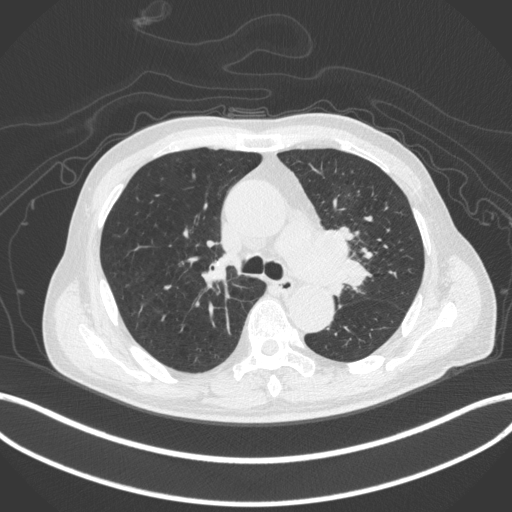
Chest CT, one axial slice; slice 285 of 420 in the series (ordered by position); 120 kVp; lung window (W 1500 / L -600 HU); 1 mm slice thickness; 512 × 512 image matrix, field of view 400 × 400 mm. Patient: male, 77 years. From the clinical record (not read from this slice): clinical TNM (as recorded): T3 N1 M0.
Structures marked on this image (bounding box drawn by a radiologist):
- lung tumour (recorded histology: adenocarcinoma): bounding box [x1, y1, x2, y2] px = [310, 227, 373, 297]